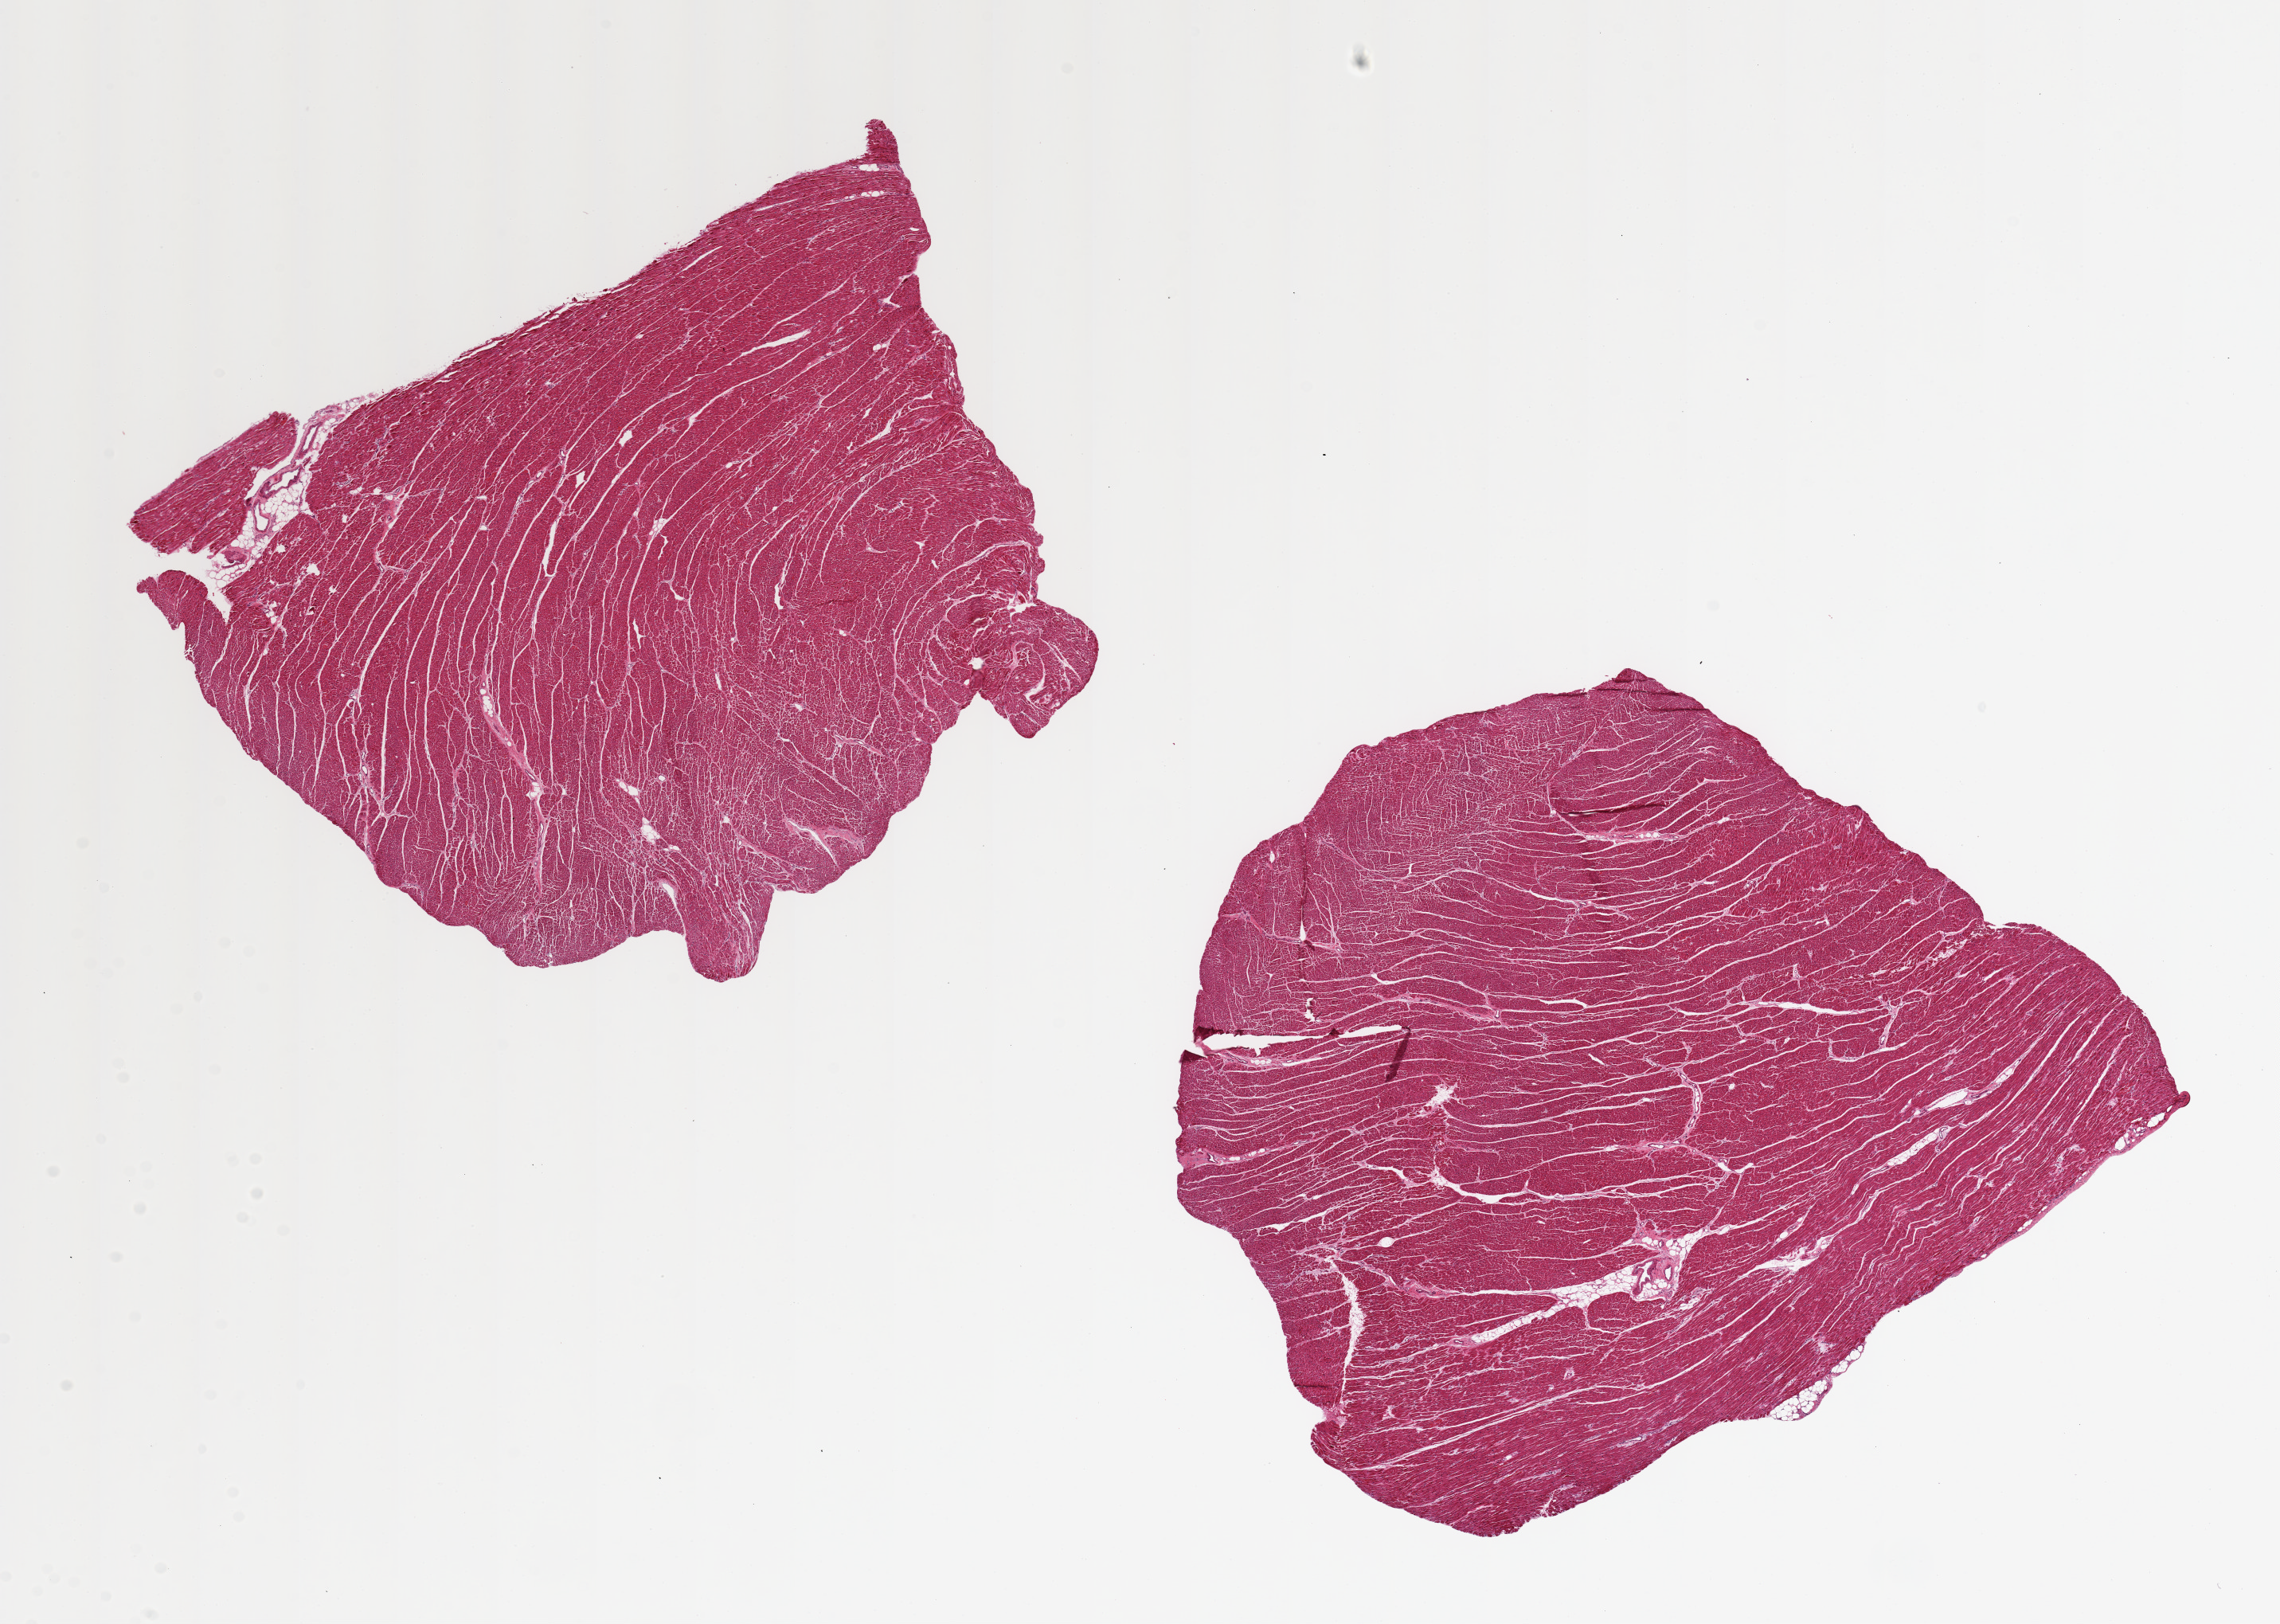
Digitized haematoxylin and eosin-stained section, low-resolution overview of the scanned area, about 22.6 x 16.1 mm. PAXgene-fixed, paraffin-embedded tissue. Sampled site (target tissue): heart. Tissue donor sample. Donor: male.
Review note (as recorded): 2 pieces ~8x7mm, minimal evident fibrosis.